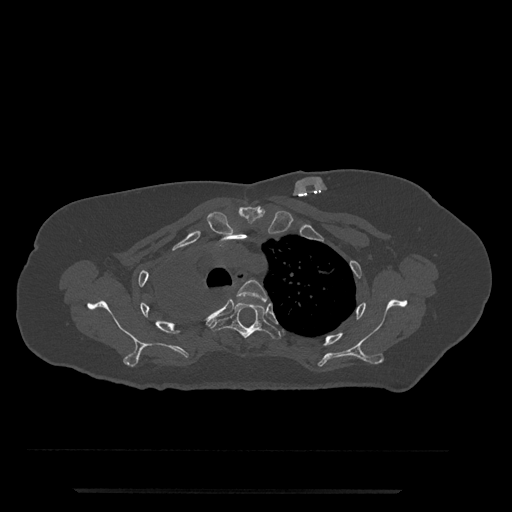
CT including the spine, one axial slice; slice 601 of 797 in the series (ordered by position); reconstruction kernel Br40s/3; bone window (W 1800 / L 400 HU); 0.5 mm slice thickness; 512 × 512 image matrix, field of view 440 × 440 mm. Patient: female, 51 years. From the clinical record (not read from this slice): primary cancer: neuro.
Outlined on this slice (semi-automatic segmentation, software-assisted and operator-edited):
- T3 vertebra: bounding box <236,279,268,302> (left, top, right, bottom; pixels)
- T4 vertebra: <210,302,281,340>